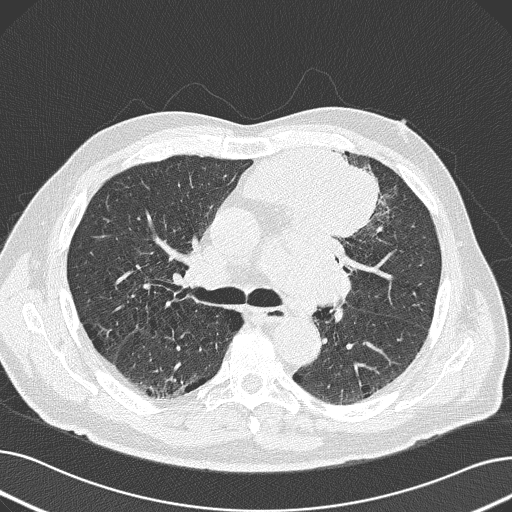
Chest CT (low-dose screening protocol), one axial image. Baseline annual screen. Lung window (W 1500 / L -600 HU). 2 mm slice thickness. Lung (sharp) reconstruction kernel (B50f). Slice 71 of 165 in the series. 512 × 512 image matrix, field of view 370 × 370 mm. Male participant, aged 69 years at enrolment. Former smoker at enrolment.
- Expert-annotated lung lesion, bounding box (x1, y1, x2, y2) in pixels: (234, 136, 384, 251).
- Reader record for this screening exam (exam-level; its link to the box is not recorded): non-calcified nodule or mass ≥4 mm, left upper lobe, 6 × 10 mm, spiculated (stellate) margins, soft tissue attenuation.
- Official screen result: positive, change unspecified: nodule(s) >= 4 mm or enlarging nodule(s), mass(es), or other non-specific abnormalities suspicious for lung cancer.